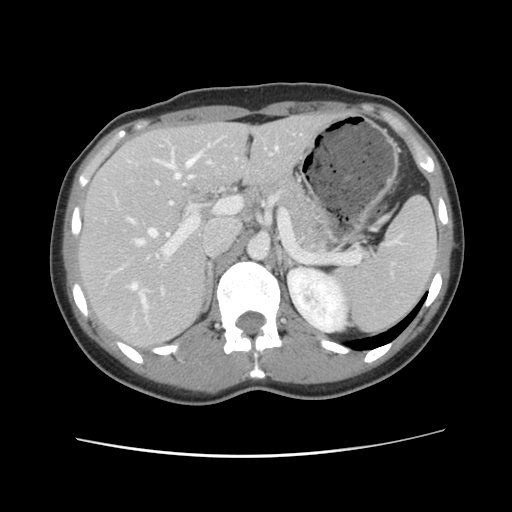
Contrast-enhanced abdominal CT, one axial slice. Slice 67 of 134 in the series (ordered by position). 120 kVp. Intravenous contrast given. Soft-tissue window (W 400 / L 40 HU). 2.5 mm slice thickness. 512 × 512 image matrix, field of view 339 × 339 mm. Female patient, age 33 years. Case-level facts recorded for this patient, not image findings: diagnosis: colorectal cancer liver metastases, imaged before liver resection; multiple liver metastases: yes; largest metastasis: 4.5 cm; disease in both lobes: yes.
Outlined on this slice (outlined manually by an expert reader):
- hepatic veins: bounding box [x1, y1, x2, y2] px = [127, 145, 279, 310]
- liver: [80, 115, 331, 350]
- planned liver remnant (the part of the liver to remain after resection): [79, 115, 332, 350]
- portal vein (with intrahepatic branches): [110, 182, 236, 297]